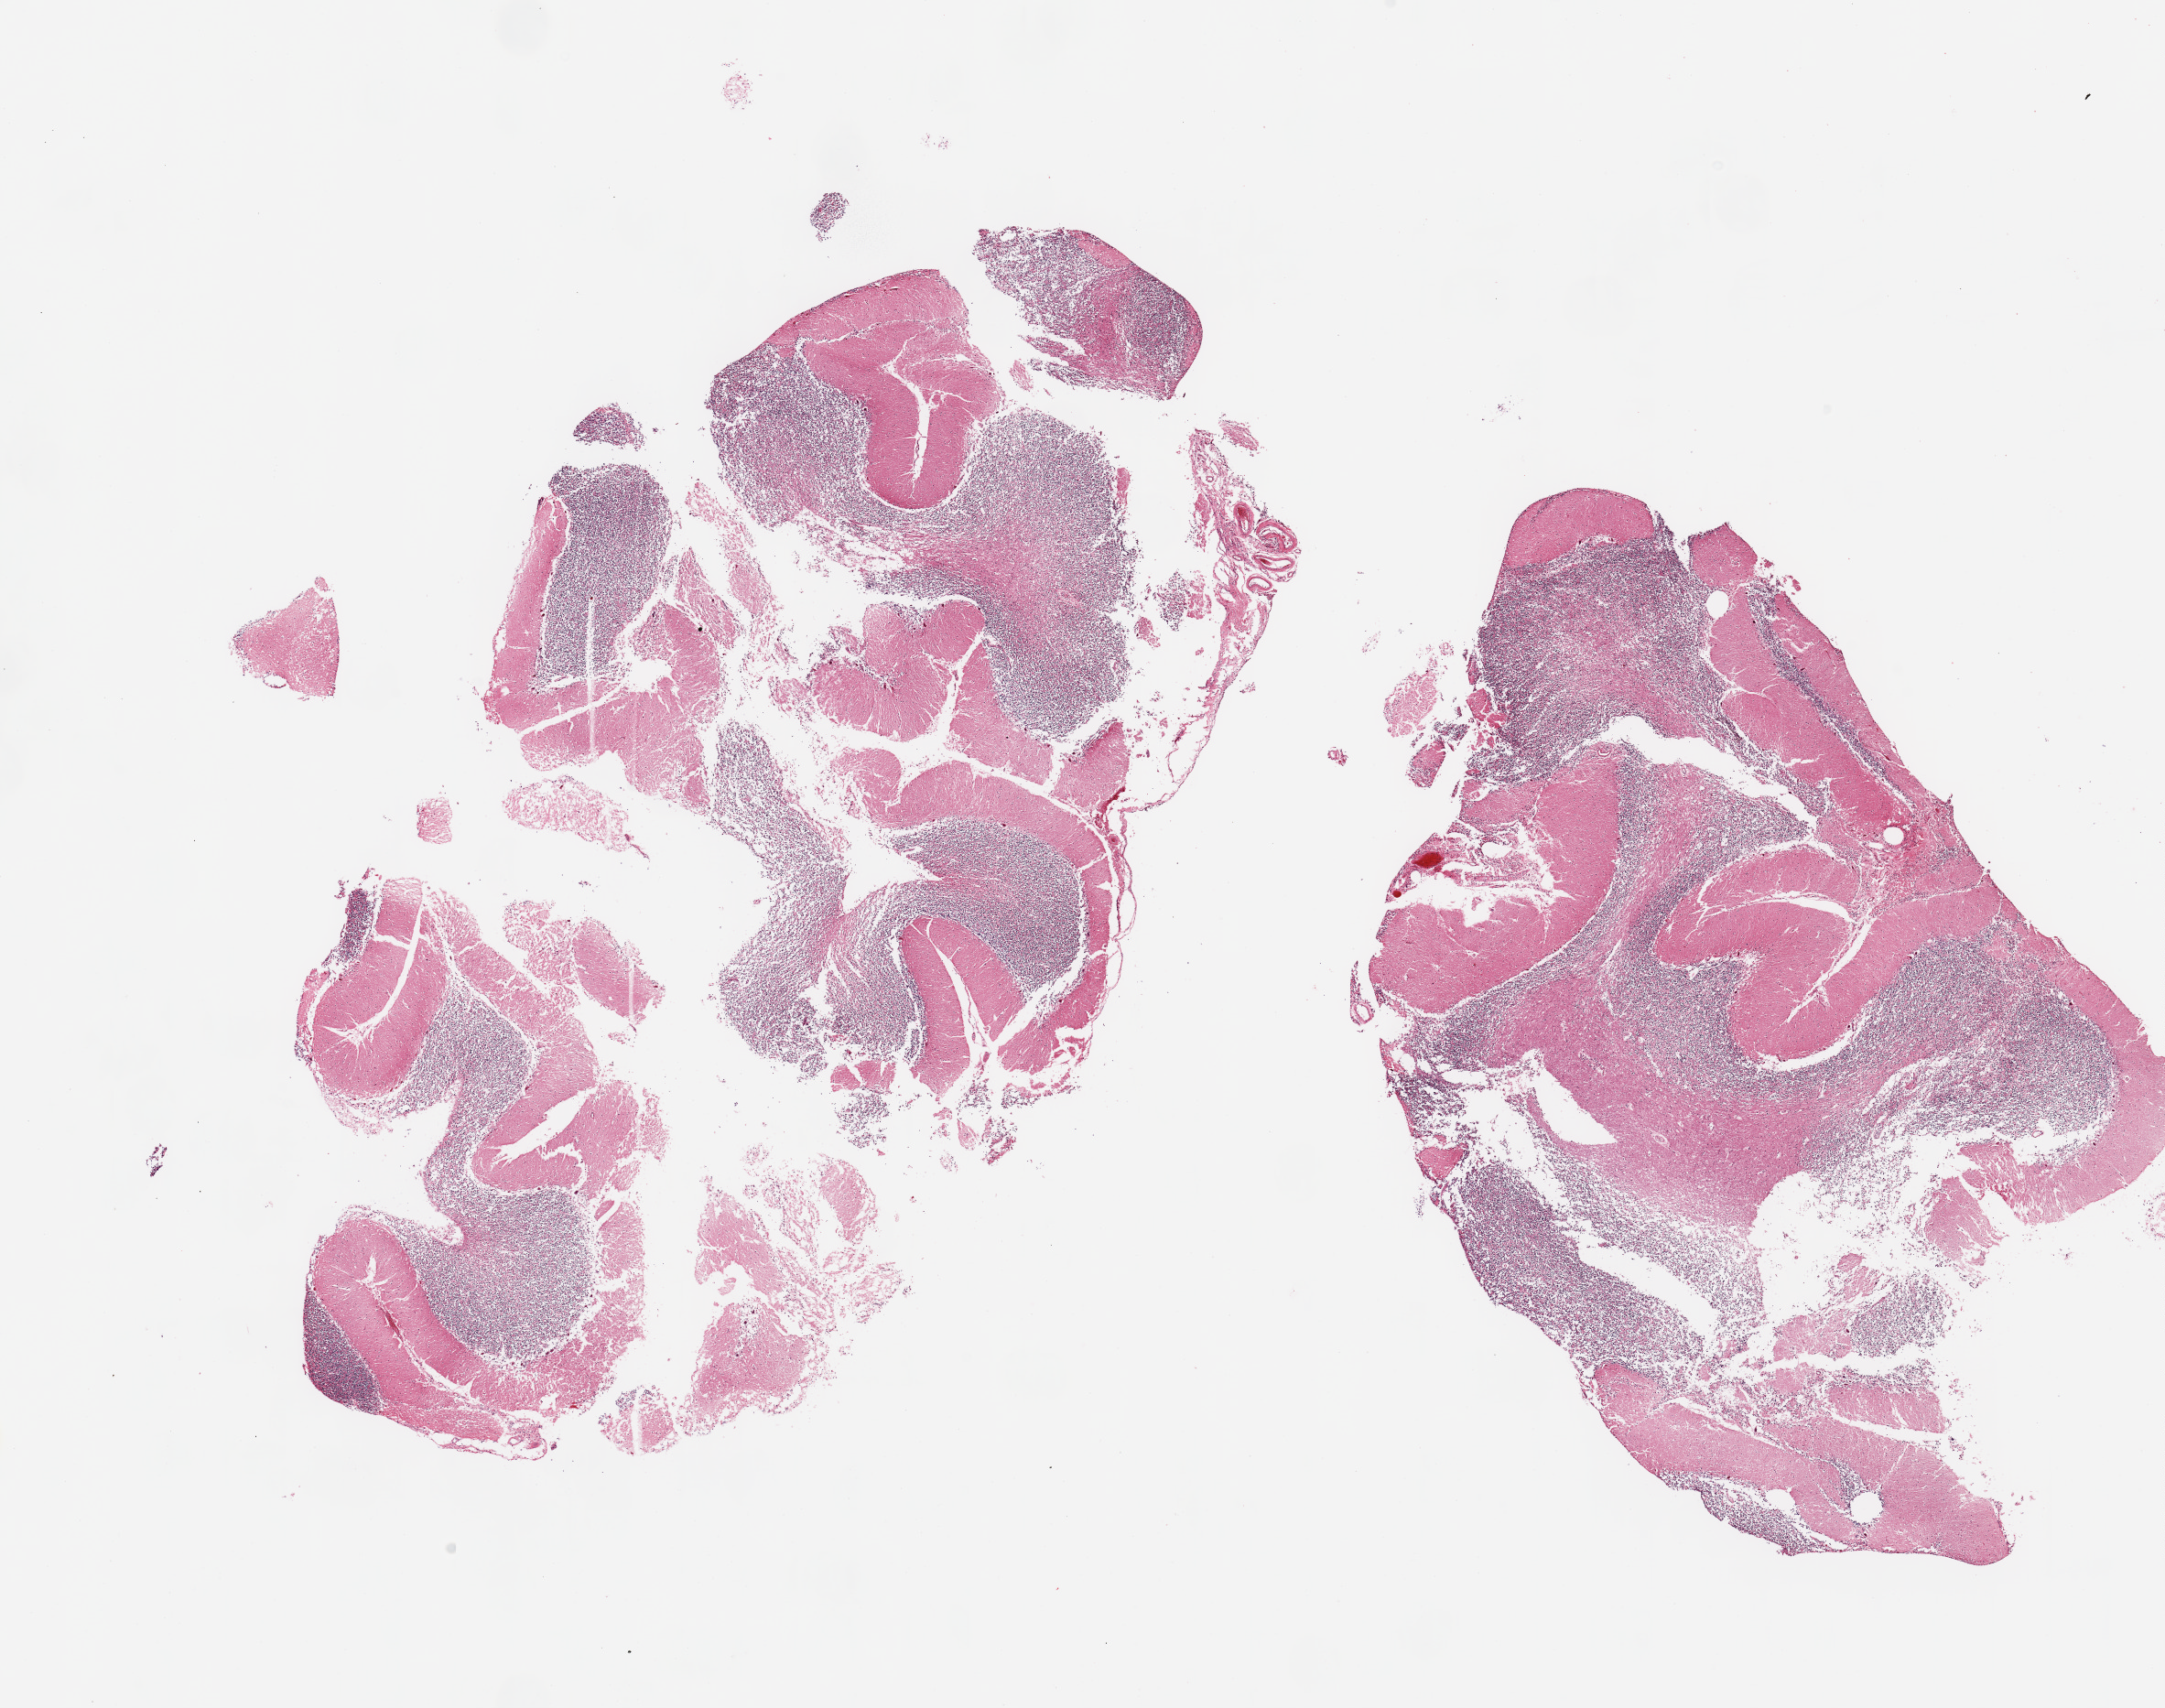
H&E whole-slide image — shown as a low-resolution overview of the whole scanned area (about 18.7 x 14.8 mm, from a 20x scan), PAXgene-fixed, paraffin-embedded tissue, target tissue: cerebellum, tissue donor sample. Donor sex: male.
Reviewer comment on this tissue sample: 2 pieces; severely autolyzed cerebellum, unable to distinguish hypoxic from autolytic changes.